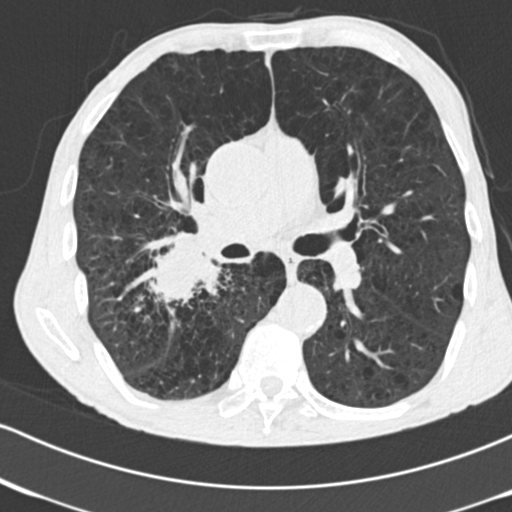
Low-dose screening chest CT, one axial slice; position 96 of 182 along the scan axis; lung window (W 1500 / L -600 HU); 2 mm slice thickness; 512 × 512 image matrix, field of view 316 × 316 mm.
Outlined on this slice (expert manual segmentation):
- lesion 1 (tumor, lower lobe of right lung): box from (x=153, y=238) to (x=222, y=305) px